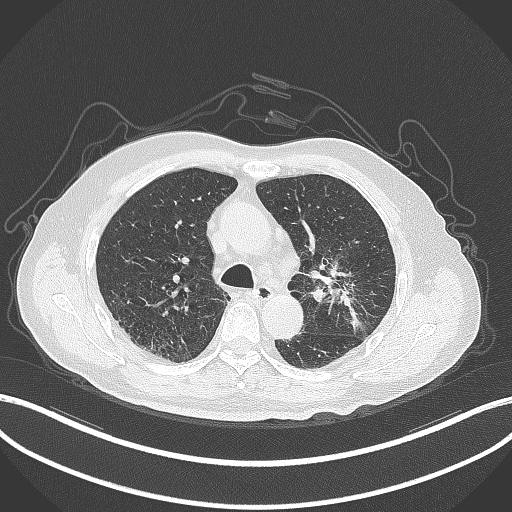
Chest CT, one axial slice; position 191 of 331 along the scan axis; reconstruction kernel B70f; 120 kVp; lung window (W 1500 / L -600 HU); 512 × 512 image matrix, field of view 400 × 400 mm. Male patient, age 79 years. From the clinical record (not read from this slice): clinical TNM (as recorded): T2a N1 M1.
Annotated regions visible in this slice (rectangle marked by the reading radiologist):
- lung tumour (recorded histology: adenocarcinoma): bounding box [x1, y1, x2, y2] px = [326, 259, 371, 339]